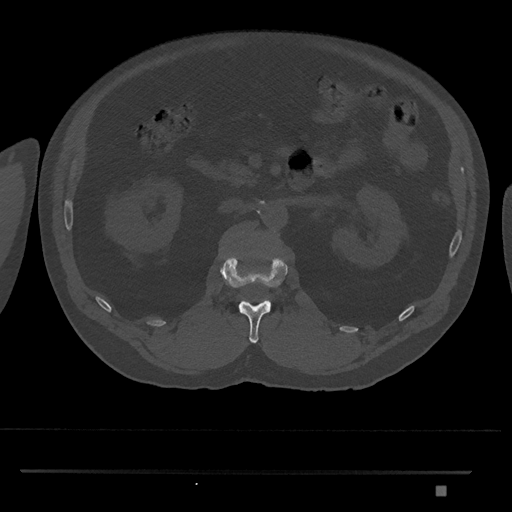
CT including the spine, one axial slice; position 802 of 1134 along the scan axis; bone window (W 1800 / L 400 HU); 0.5 mm slice thickness; 512 × 512 image matrix, field of view 429 × 429 mm. Male patient, age 65 years. From the clinical record (not read from this slice): primary cancer: prostate.
Outlined on this slice (semi-automatic segmentation, software-assisted and operator-edited):
- L1 vertebra: bounding box [x1, y1, x2, y2] px = [220, 254, 288, 343]